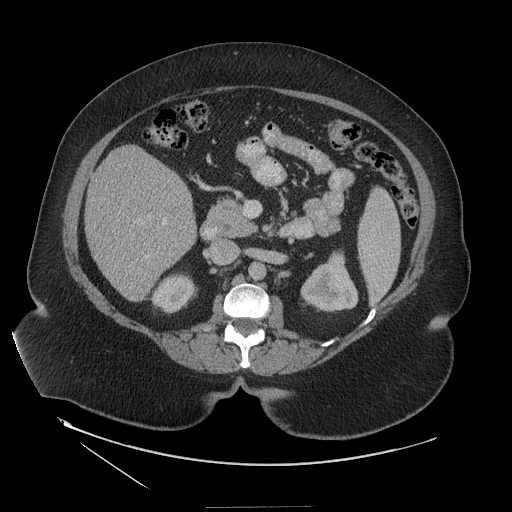
Contrast-enhanced abdominal CT (liver protocol), one axial slice; position 55 of 127 along the scan axis; reconstruction kernel STANDARD; soft-tissue window (W 400 / L 40 HU); 512 × 512 image matrix. Case-level facts recorded for this patient, not image findings: diagnosis: hepatocellular carcinoma (patient treated with transarterial chemoembolisation; whether this scan precedes or follows treatment is not stated here); TNM stage (as recorded): Stage-II; Child-Pugh class: A; tumour differentiation: well differentiated; tumour nodularity: multinodular.
Structures marked on this image (semi-automatic segmentation, software-assisted and operator-edited):
- liver parenchyma outside the tumour (the mass and vessels are separate outlines, so this box may not span the whole liver): box from (x=84, y=145) to (x=196, y=300) px
- liver vessels: (x=146, y=222)–(x=165, y=258)